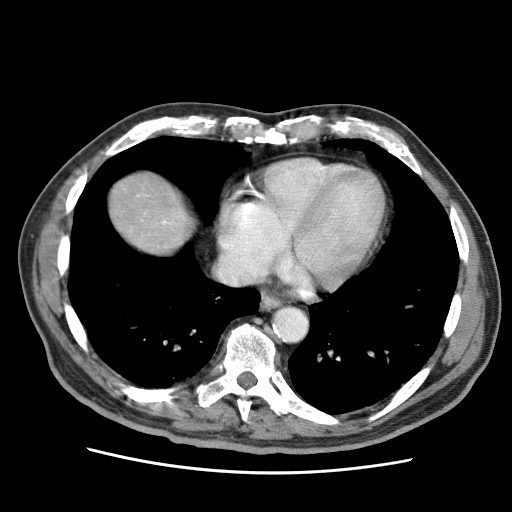
Contrast-enhanced abdominal CT (liver protocol), one axial slice. Position 65 of 75 along the scan axis. 120 kVp. Soft-tissue window (W 400 / L 40 HU). 2.5 mm slice thickness. 512 × 512 image matrix, field of view 360 × 360 mm. From the clinical record (not read from this slice): diagnosis: hepatocellular carcinoma (patient treated with transarterial chemoembolisation; whether this scan precedes or follows treatment is not stated here); TNM stage (as recorded): Stage-IIIA; Child-Pugh class: A; tumour differentiation: well differentiated.
Structures marked on this image (semi-automatically segmented with operator editing):
- liver parenchyma outside the tumour (the mass and vessels are separate outlines, so this box may not span the whole liver): bounding box <110,172,190,252> (left, top, right, bottom; pixels)
- liver vessels: <161,220,172,225>